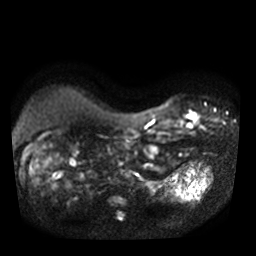
Breast MRI, one axial slice; diffusion-weighted series; image 2 of 4 stored at this slice position (different b-values; order by instance number); 3 T; 5 mm slice thickness; 256 × 256 image matrix, field of view 320 × 320 mm. Female patient.
Annotated regions visible in this slice (manually delineated by an expert):
- tumour on diffusion-weighted imaging: bounding box (x1, y1, x2, y2) in pixels: (187, 114, 198, 121)